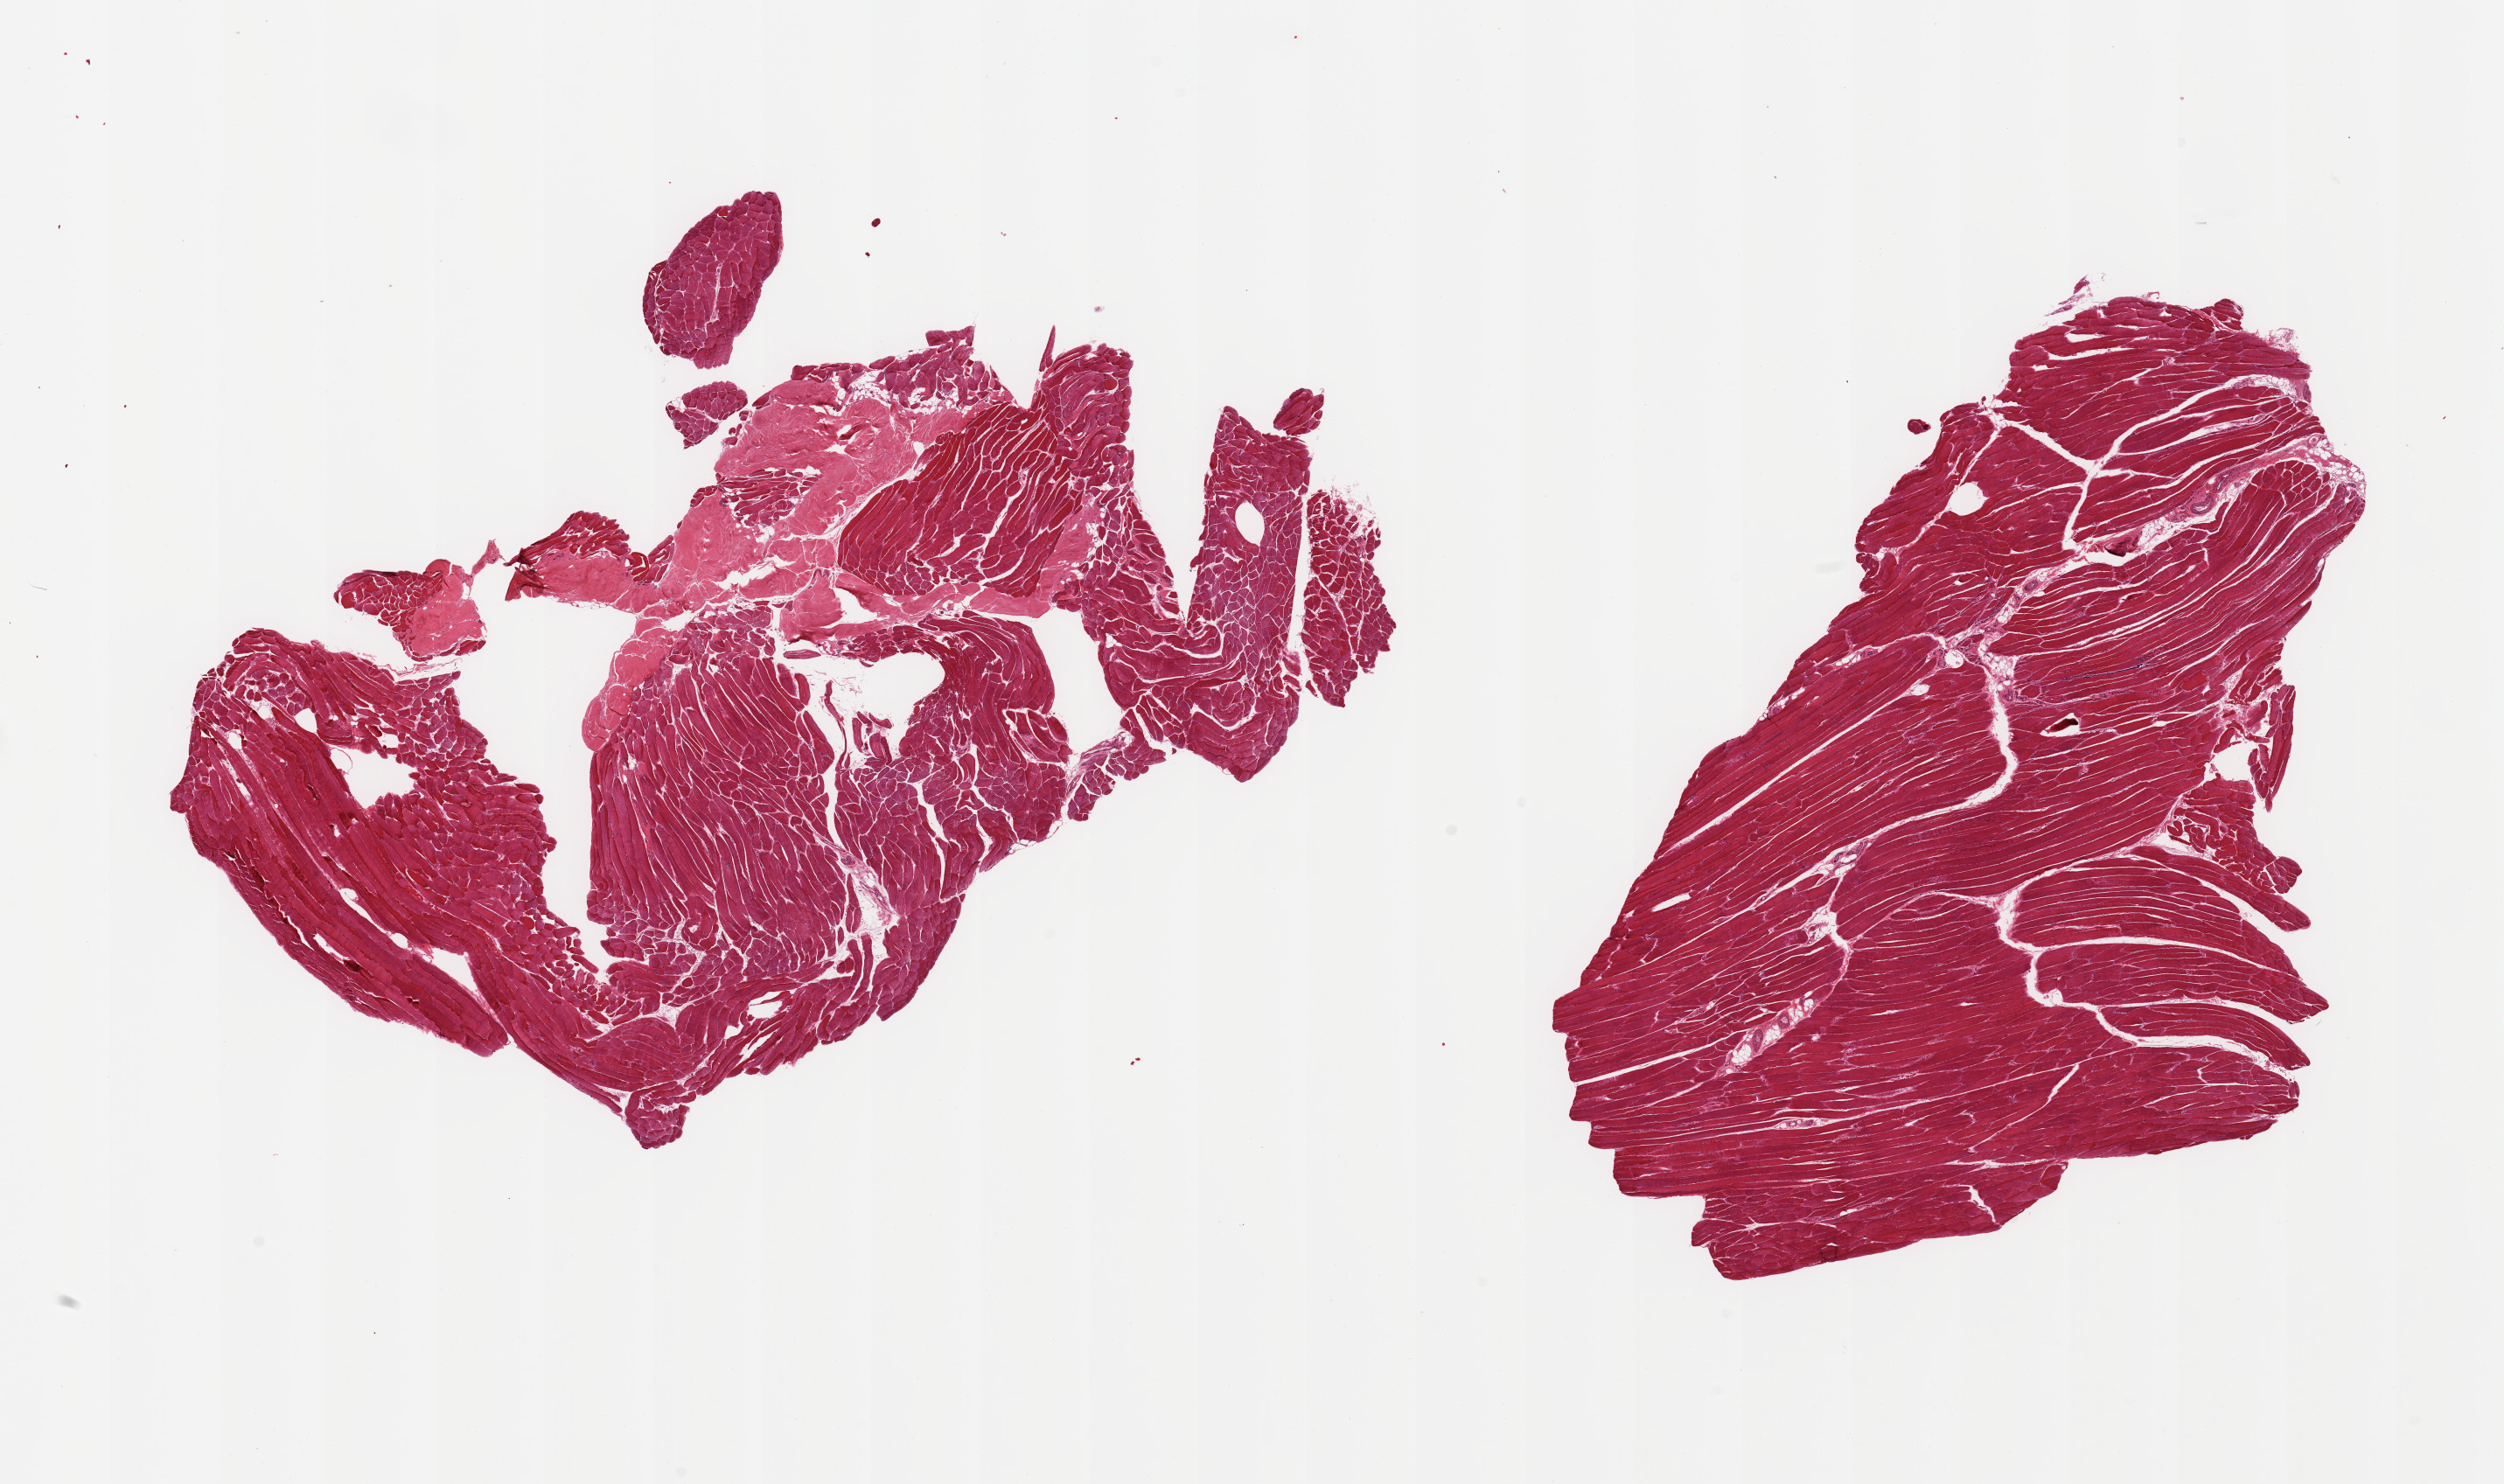
H&E whole-slide image, brightfield, a low-resolution overview of the entire scanned area, about 22.6 x 13.4 mm; PAXgene-fixed, paraffin-embedded tissue; section of skeletal muscle (target tissue); tissue donor sample. Donor: male.
Reviewer comment on this tissue sample: 2 pieces, !0% tendinous insertion/interstitial fat.